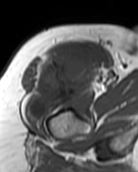
MRI of an extremity soft-tissue mass, one axial slice. Slice 78 of 99 in the series (ordered by position). MR volume resampled by the dataset authors to the PET/CT grid (not the native acquisition matrix). 3.27 mm slice thickness. 138 × 172 image matrix, field of view 135 × 168 mm. Female patient. Case-level facts recorded for this patient, not image findings: histological type: pleiomorphic undifferentiated sarcoma; grade: high; site of the primary tumour: right quadricep.
Structures marked on this image (expert contour drawn on MRI and transferred to this co-registered scan by the dataset authors):
- gross tumour volume including surrounding oedema: bounding box <26,50,95,119> (left, top, right, bottom; pixels)
- gross tumour volume (mass): <26,50,95,119>